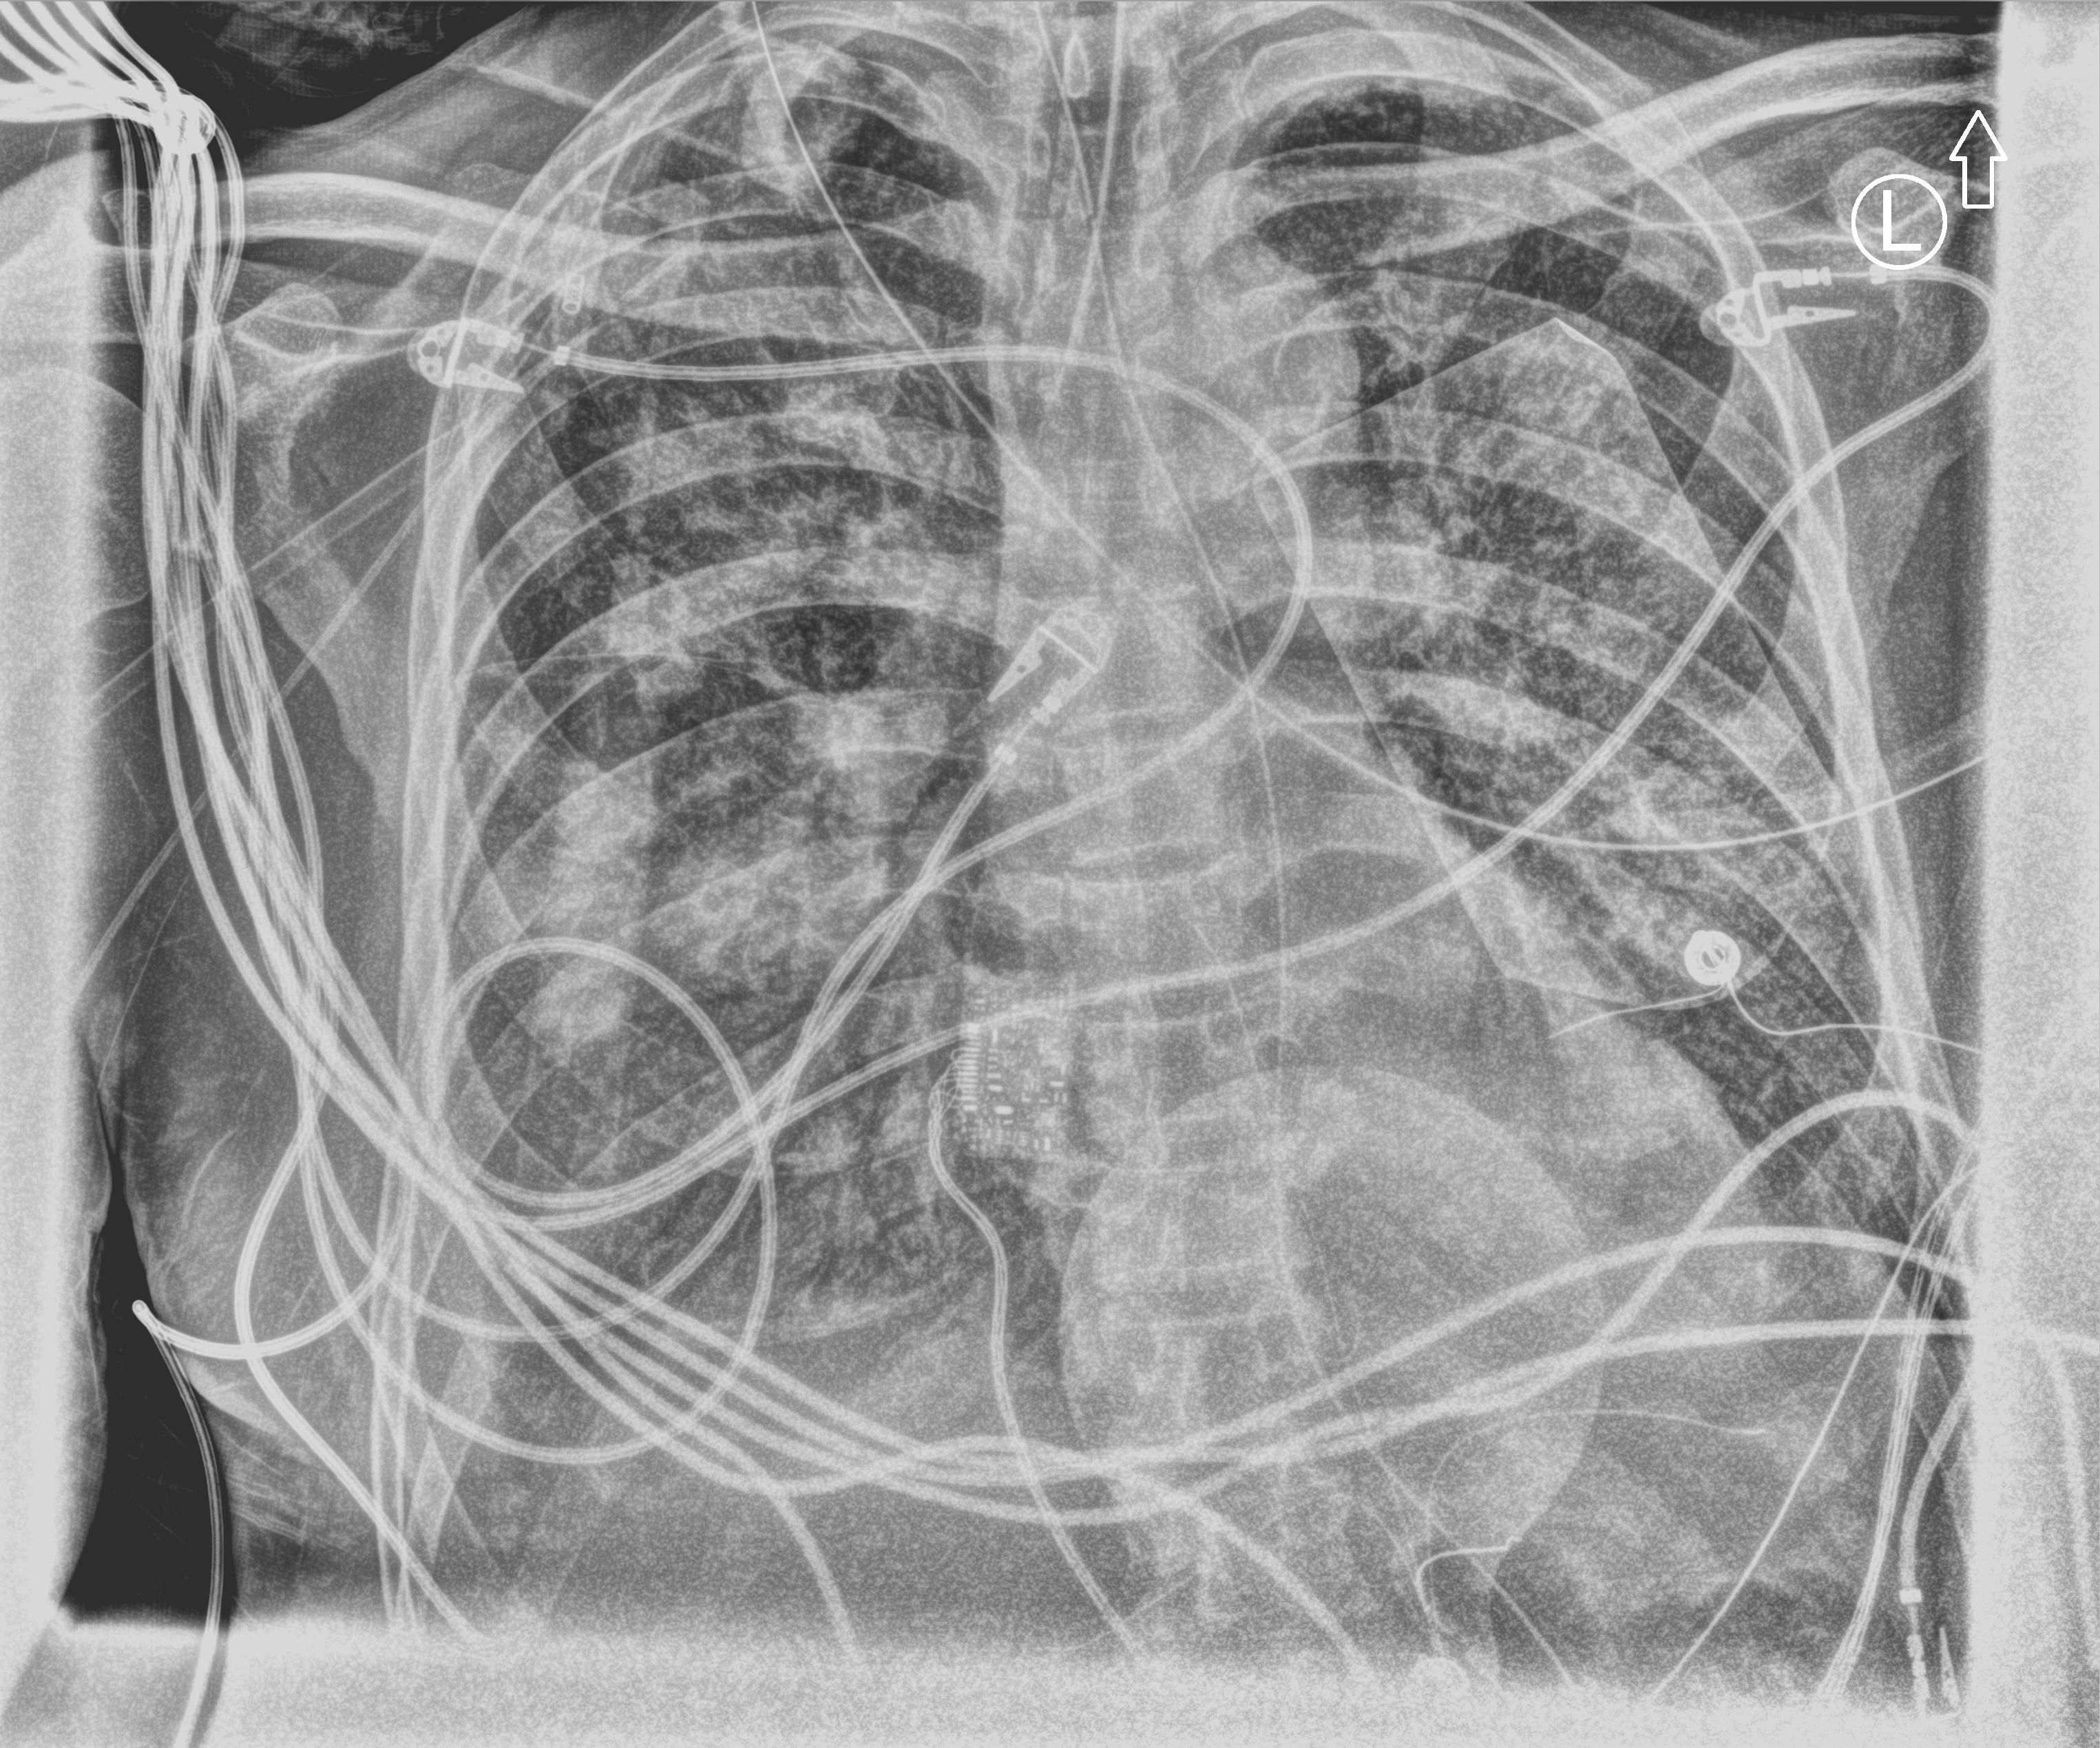
Chest X-ray (portable), anteroposterior (AP) projection. Male patient hospitalised with COVID-19, age 60–74 years.
From the hospital-stay record, not from the radiograph (when in the stay this image was taken is not recorded): length of hospital stay: 31 days.